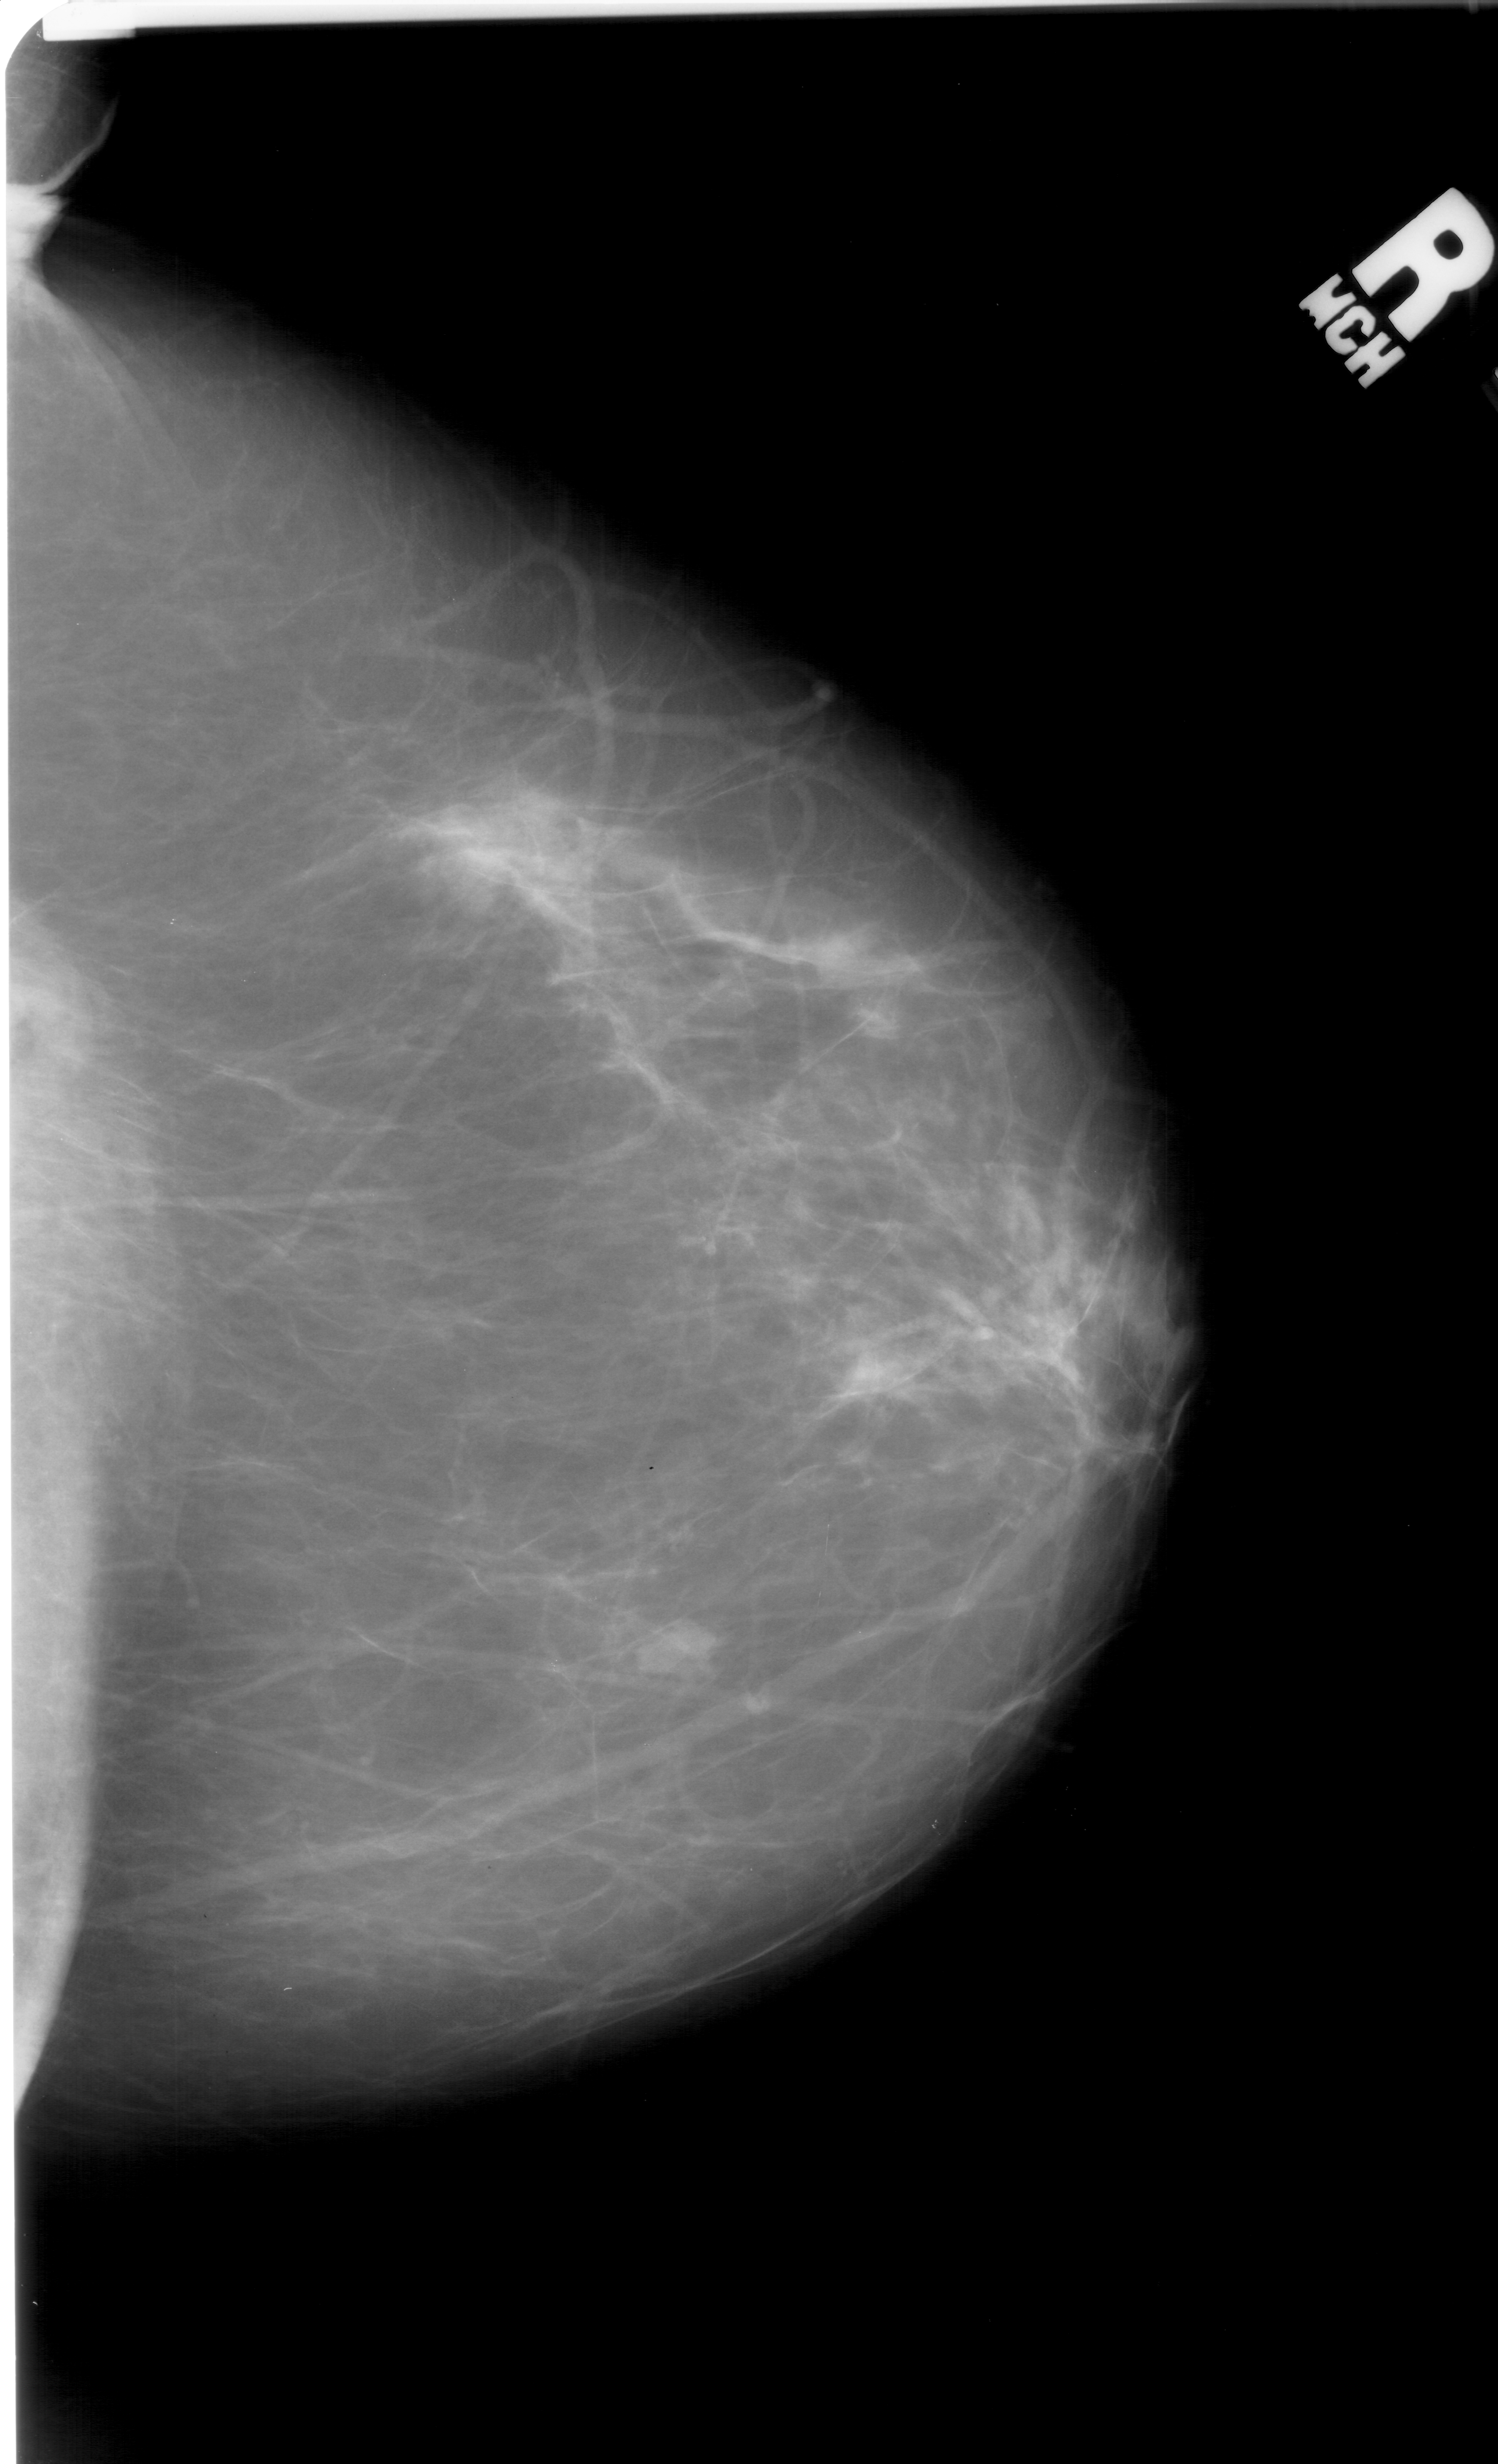
Scanned film-screen mammogram, right breast, craniocaudal (CC) view, BI-RADS breast density category 2 (scale 1–4).
Finding: mass, shape lobulated, margins ill defined; BI-RADS assessment category 4; pathology result (as recorded, not read from the image): malignant.